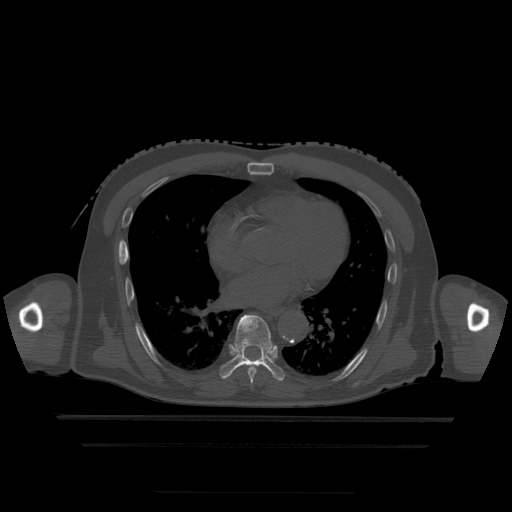
CT including the spine, one axial slice. Position 286 of 522 along the scan axis. Bone window (W 1800 / L 400 HU). 1.25 mm slice thickness. 512 × 512 image matrix, field of view 436 × 436 mm. Patient age 68 years. Case-level facts recorded for this patient, not image findings: primary cancer: urothelial.
Annotated regions visible in this slice (semi-automatically segmented with operator editing):
- T6 vertebra: bounding box <251,383,253,387> (left, top, right, bottom; pixels)
- T7 vertebra: <248,366,259,383>
- T8 vertebra: <220,315,285,381>